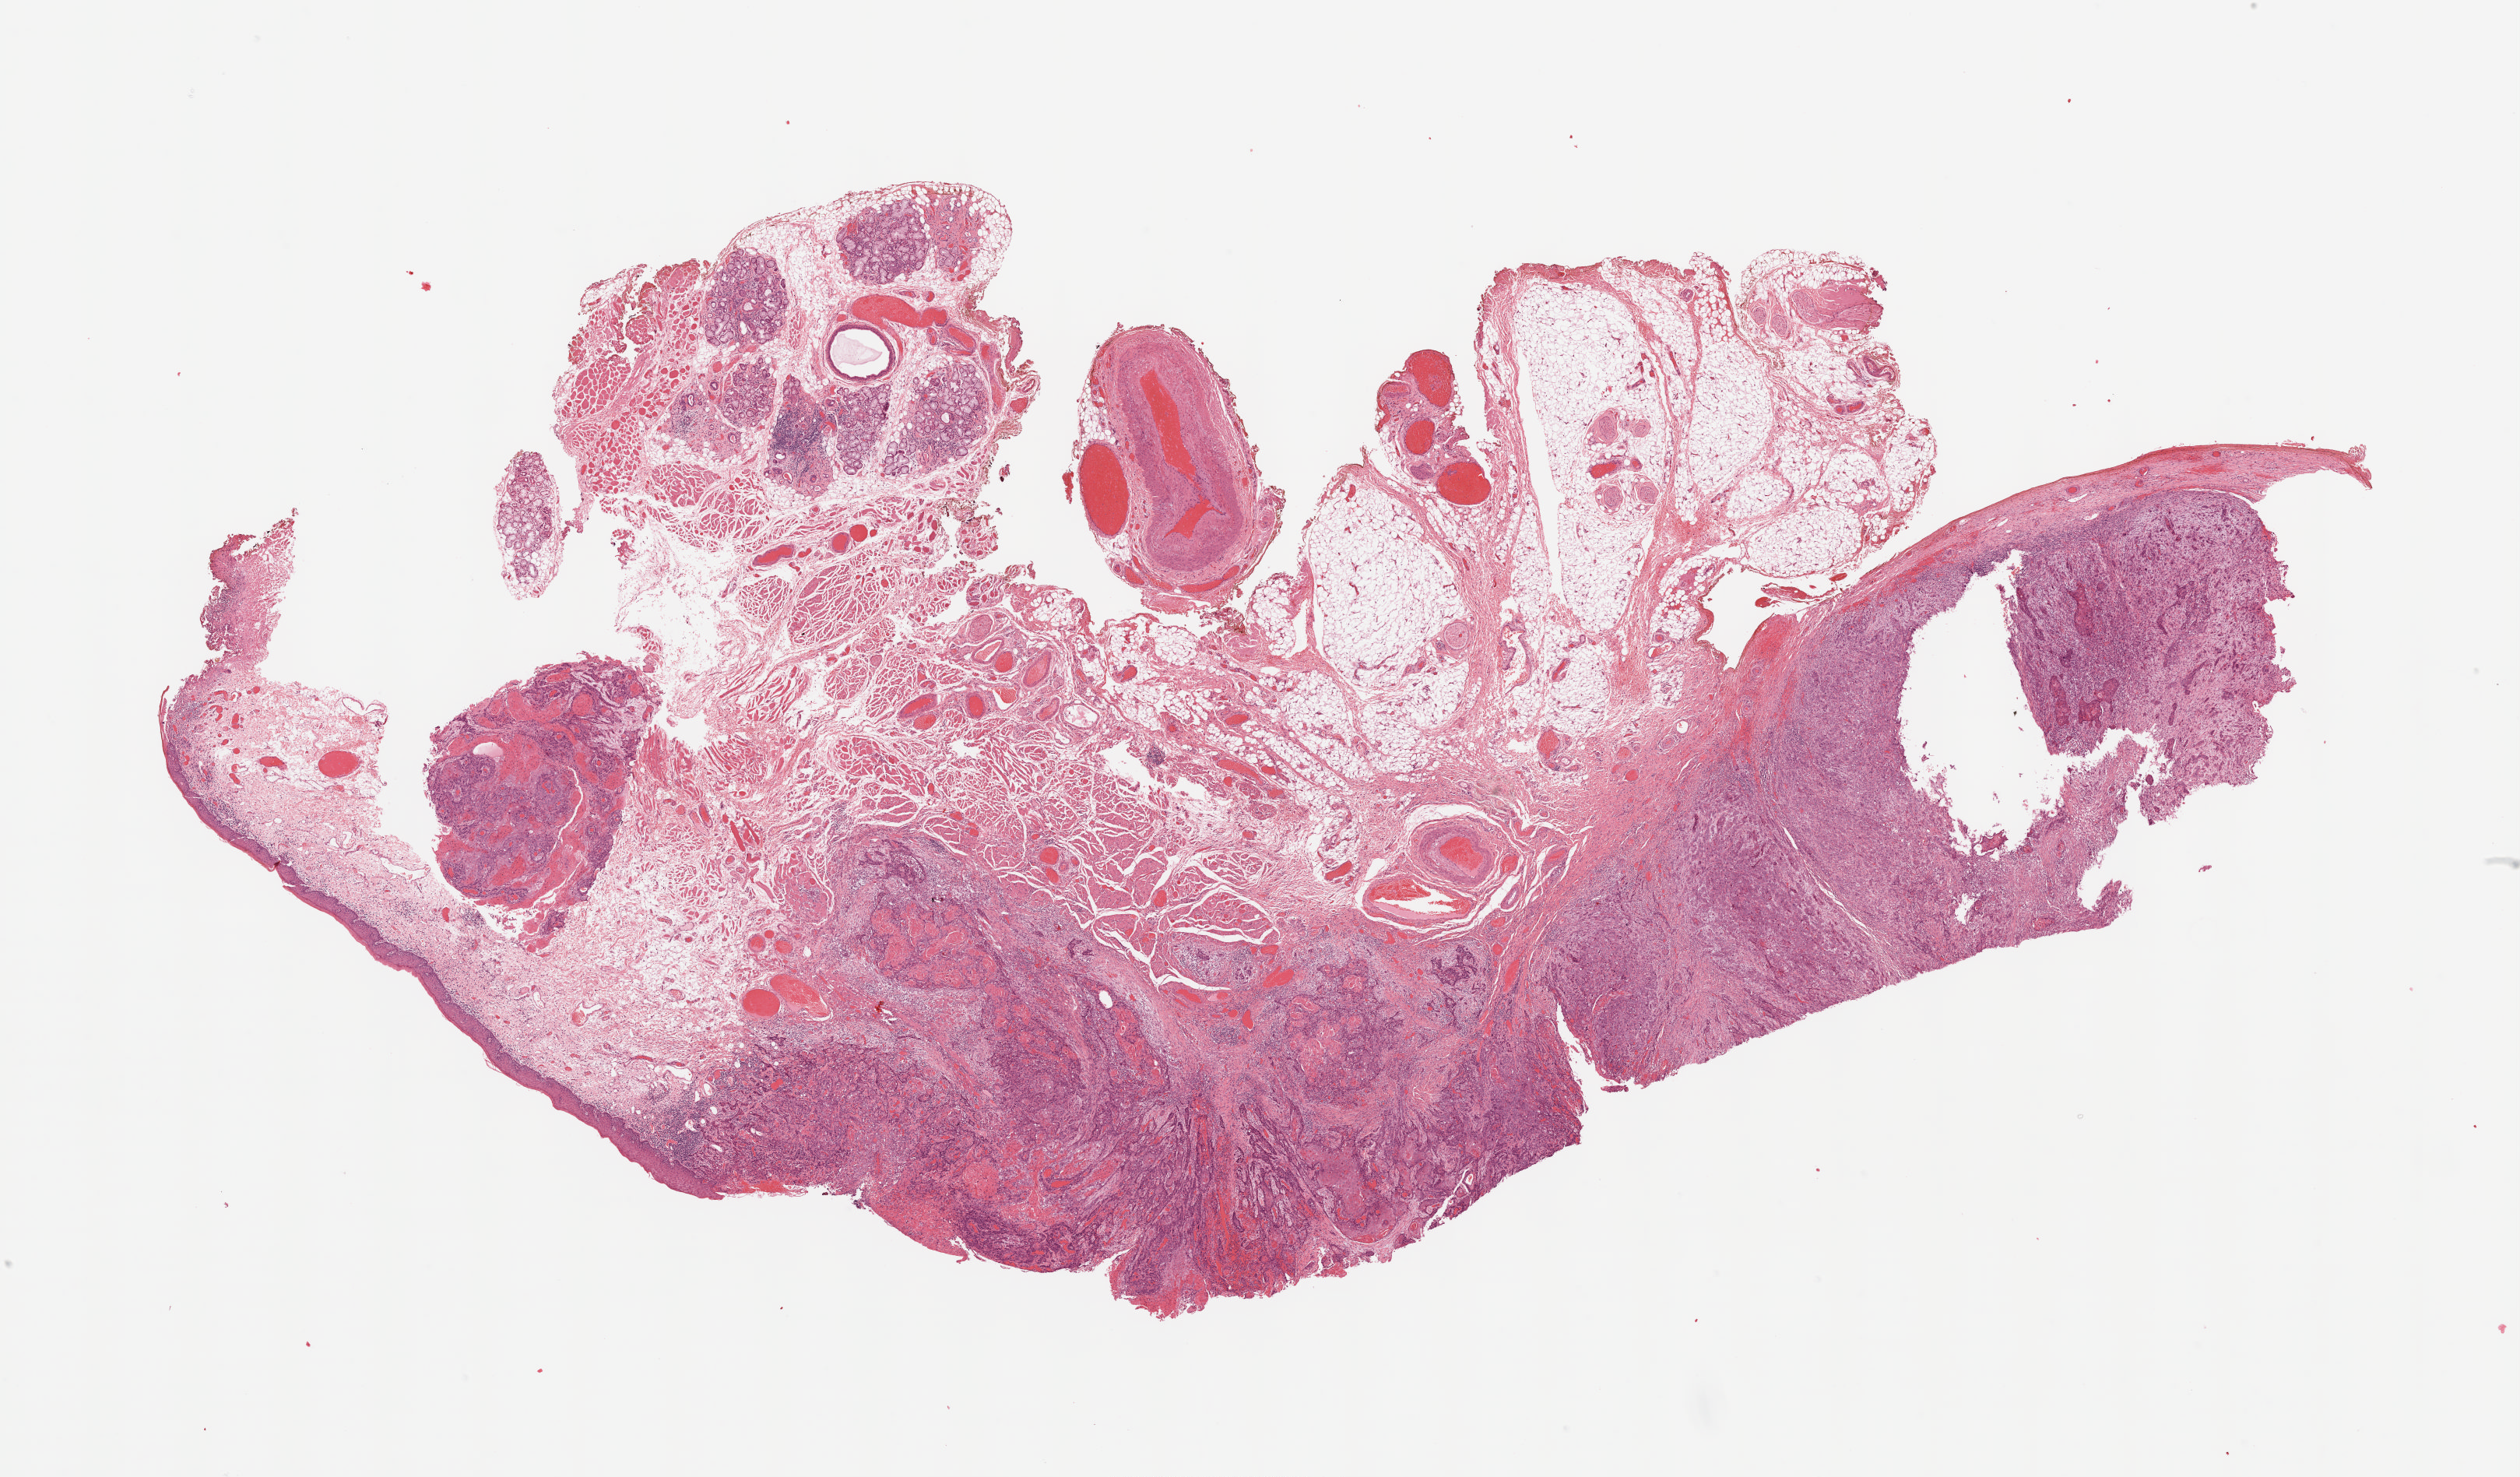
Digitized H&E-stained tissue section (whole slide) — shown as a low-resolution overview of the whole scanned area (about 26.0 x 15.2 mm). Formalin-fixed paraffin-embedded (FFPE) diagnostic section. Head and neck, primary tumour sample. Male, age 88 years at initial diagnosis. Histologic grade: G3 (poorly differentiated).
• pathologic diagnosis: Squamous cell carcinoma, NOS (floor of mouth, NOS)
• AJCC pathologic stage: III (7th edition)
• laterality: left